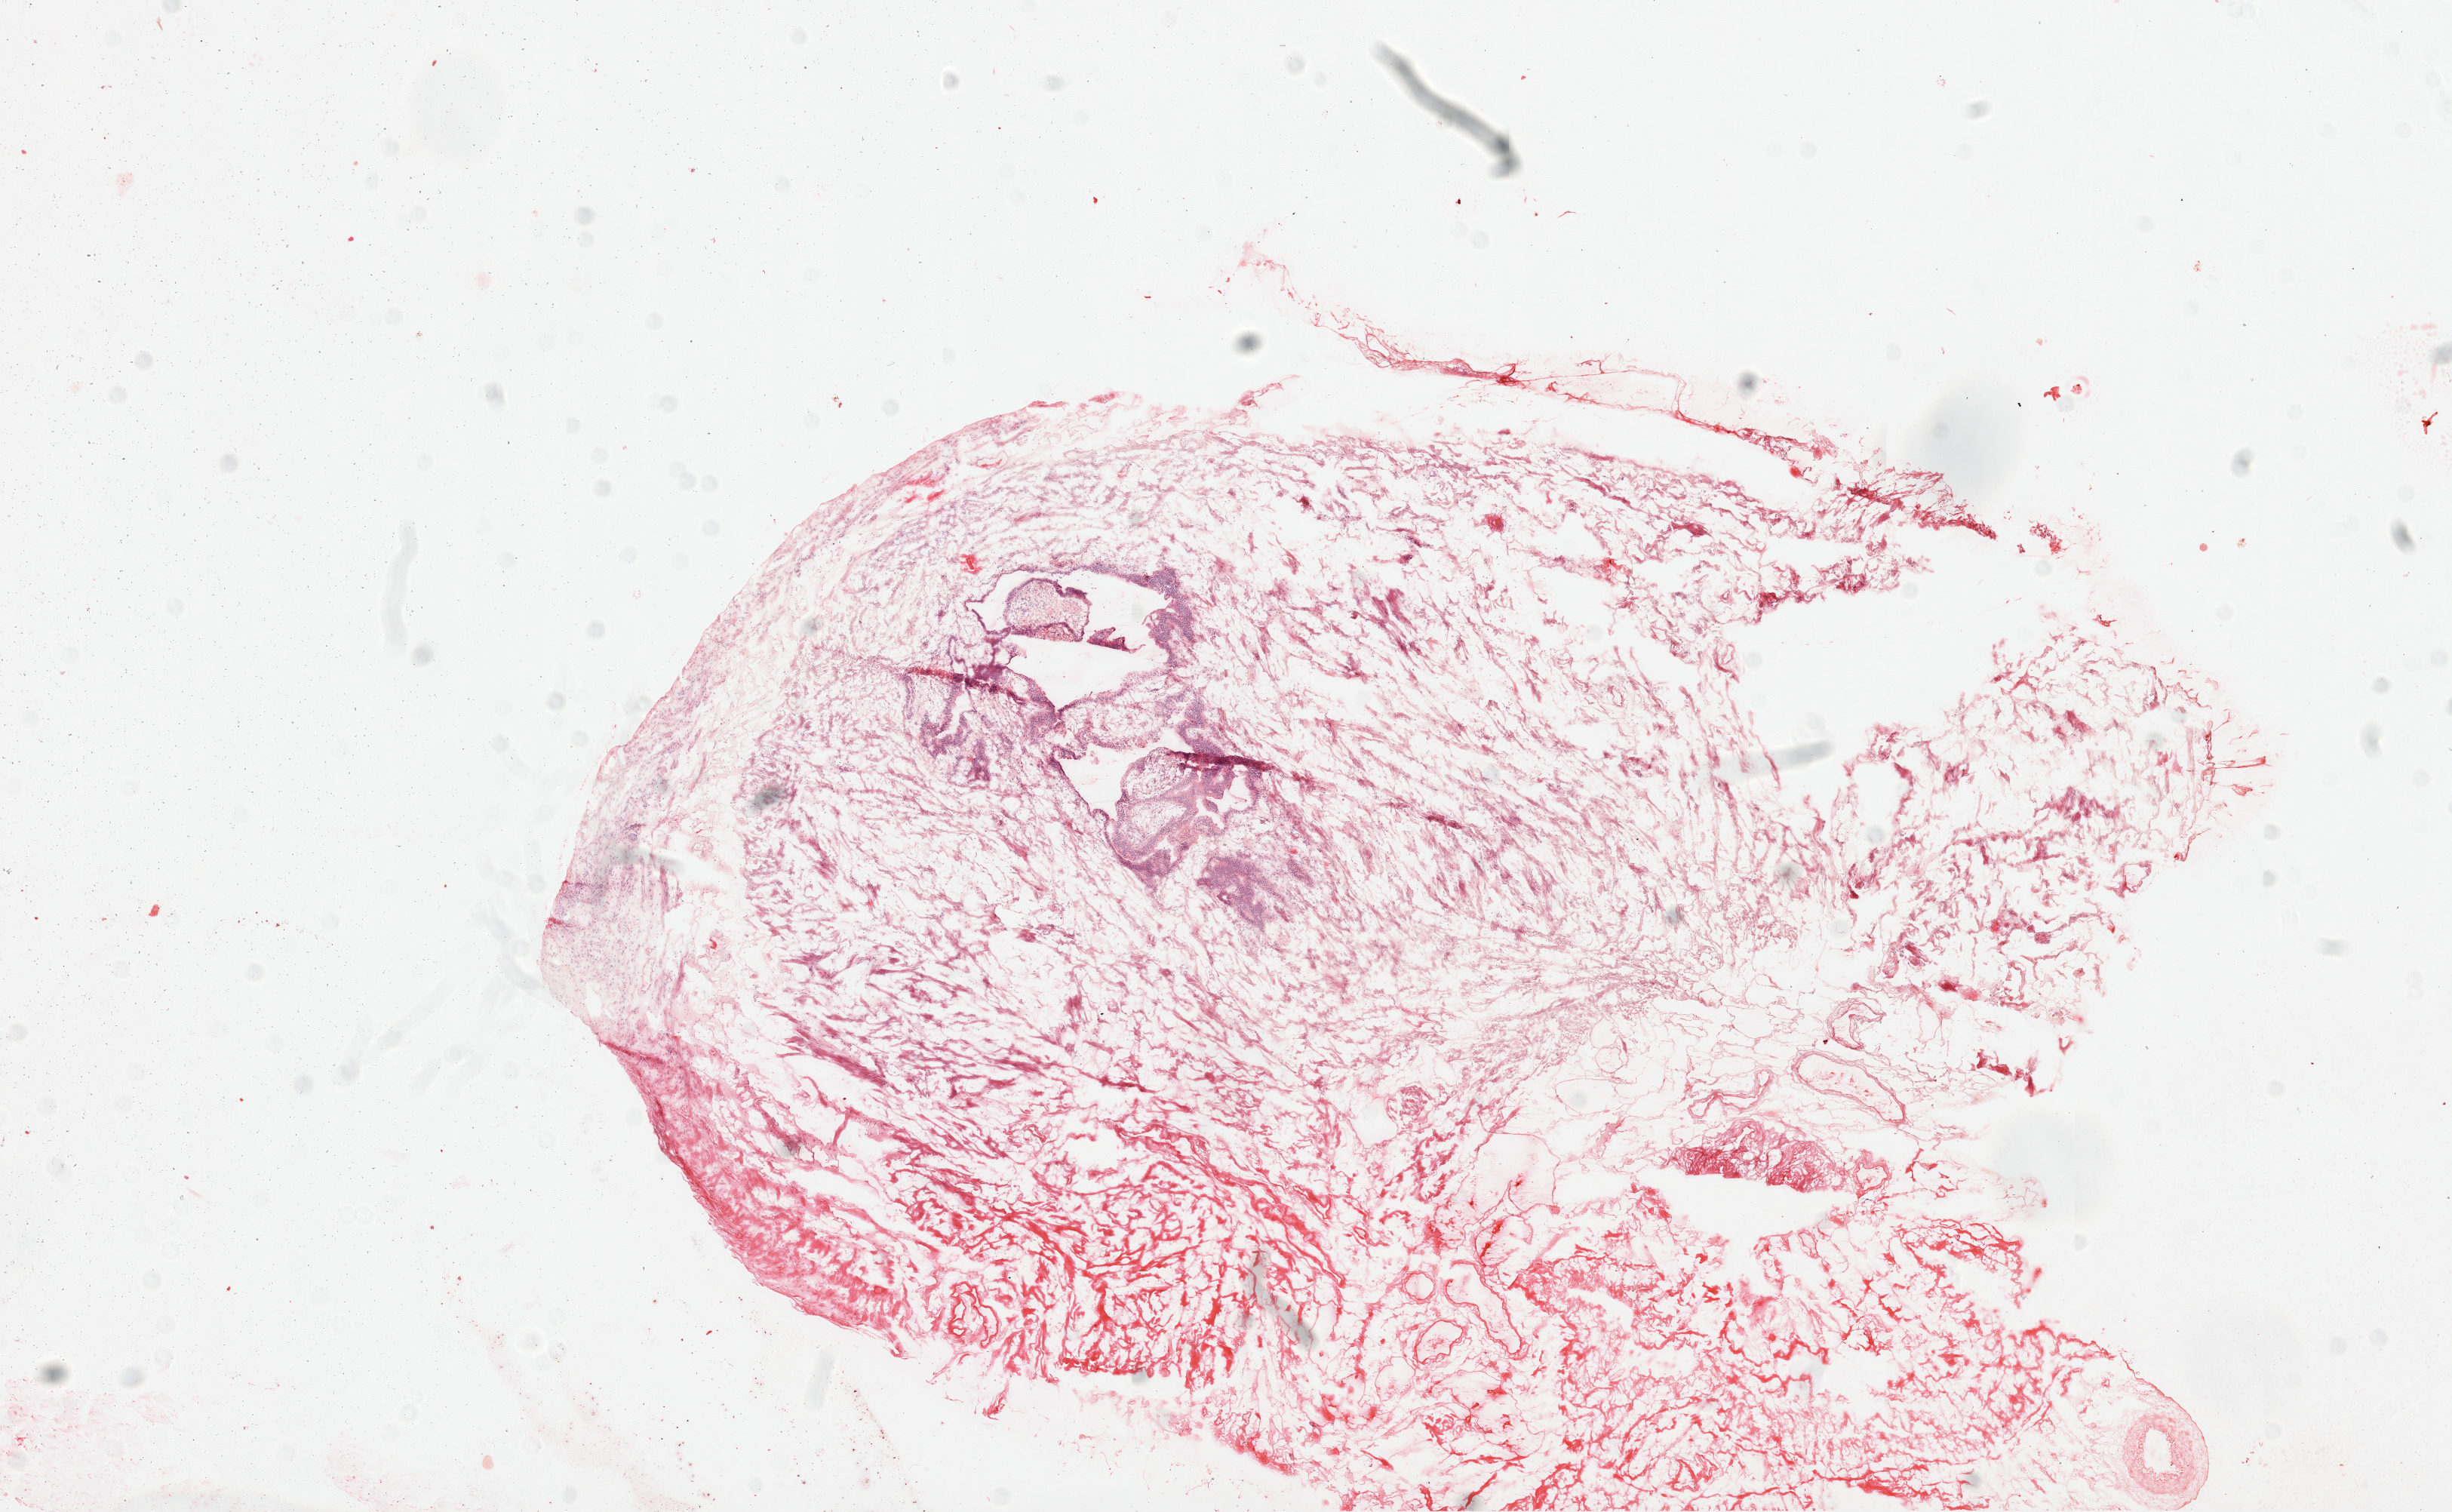
Whole-slide histology image, H&E-stained — whole scanned area (about 13.0 x 8.0 mm) shown as a low-resolution overview; frozen section from the top of the tissue portion; sample: solid tissue normal (non-tumour tissue), ovary. Female patient; age at initial diagnosis 62 years.
This section: solid tissue normal sample (biorepository sample class). Patient diagnosis: Serous cystadenocarcinoma, NOS.